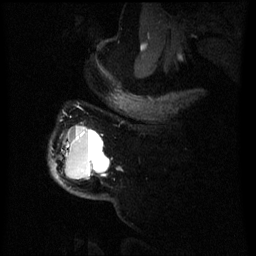
Breast MRI (dynamic contrast-enhanced), one sagittal slice. Dynamic contrast-enhanced series, image 2 of 3 at this slice position (ordered by acquisition). 1.5 T. TE 4.2 ms, TR 8 ms. 256 × 256 image matrix. Patient: female, 50 years.
Outlined on this slice (semi-automatic segmentation, software-assisted and operator-edited):
- analysis volume of interest (the breast-tissue region the enhancement analysis was run in; not a lesion): bounding box [x1, y1, x2, y2] px = [52, 126, 110, 183]
- tumour enhancement mask (voxels above the 70 % enhancement threshold inside the analysis volume of interest): [74, 136, 106, 177]